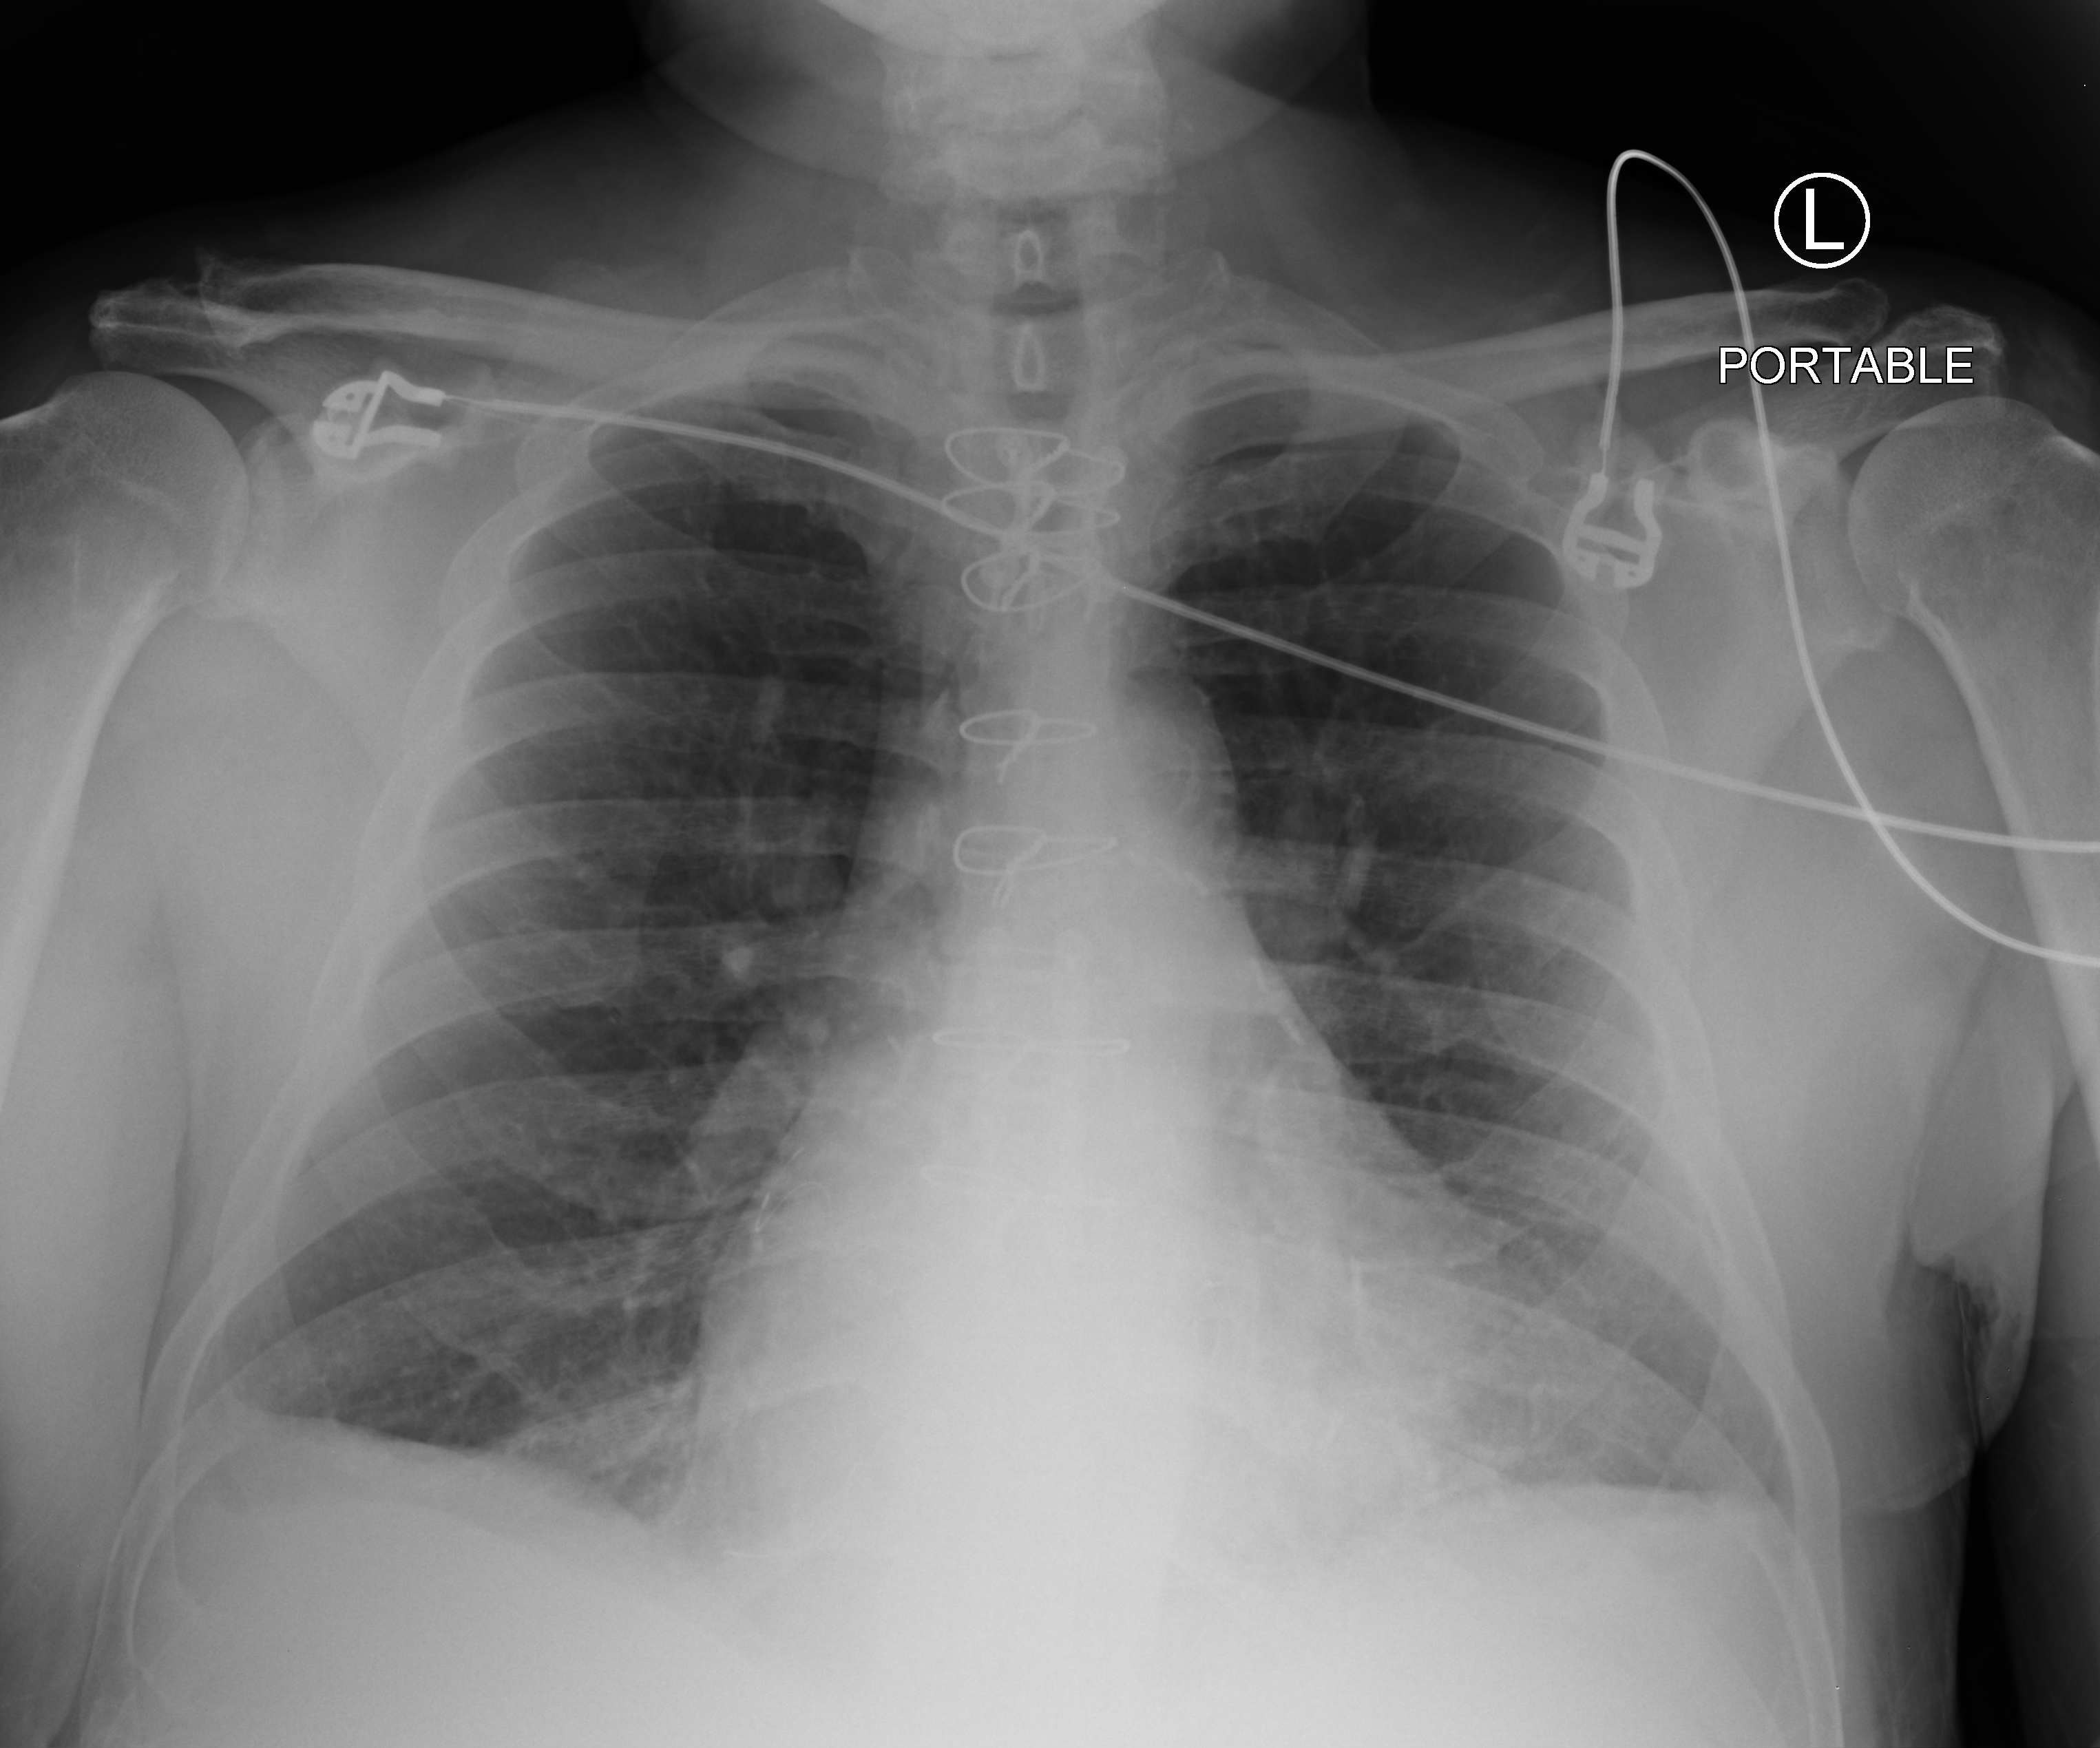
Chest X-ray (portable), anteroposterior (AP) projection. Patient hospitalised with COVID-19; male, aged 60–74 years.
Admission-level facts for this patient (not findings on this image; timing relative to this image not recorded):
- mechanically ventilated during this hospital stay: no
- COPD (admission record): no
- admitted to intensive care during this hospital stay: no